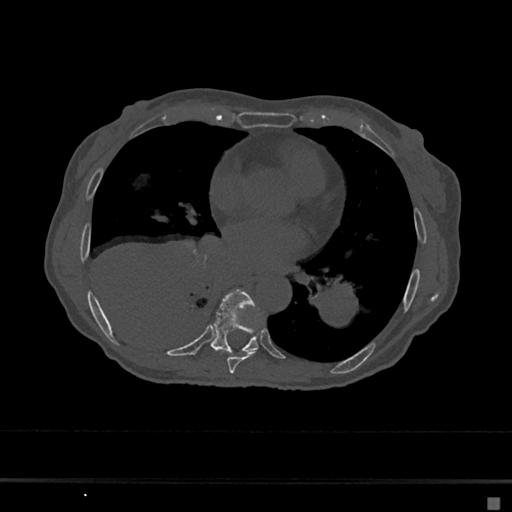
CT including the spine, one axial slice; slice 346 of 797 in the series (ordered by position); 120 kVp; bone window (W 1800 / L 400 HU); 0.5 mm slice thickness; 512 × 512 image matrix. Female patient, age 68 years. Case-level facts recorded for this patient, not image findings: primary cancer: renal.
Annotated regions visible in this slice (semi-automatic segmentation, software-assisted and operator-edited):
- T7 vertebra: bounding box (x1, y1, x2, y2) in pixels: (227, 351, 256, 374)
- T8 vertebra: (211, 290, 259, 355)